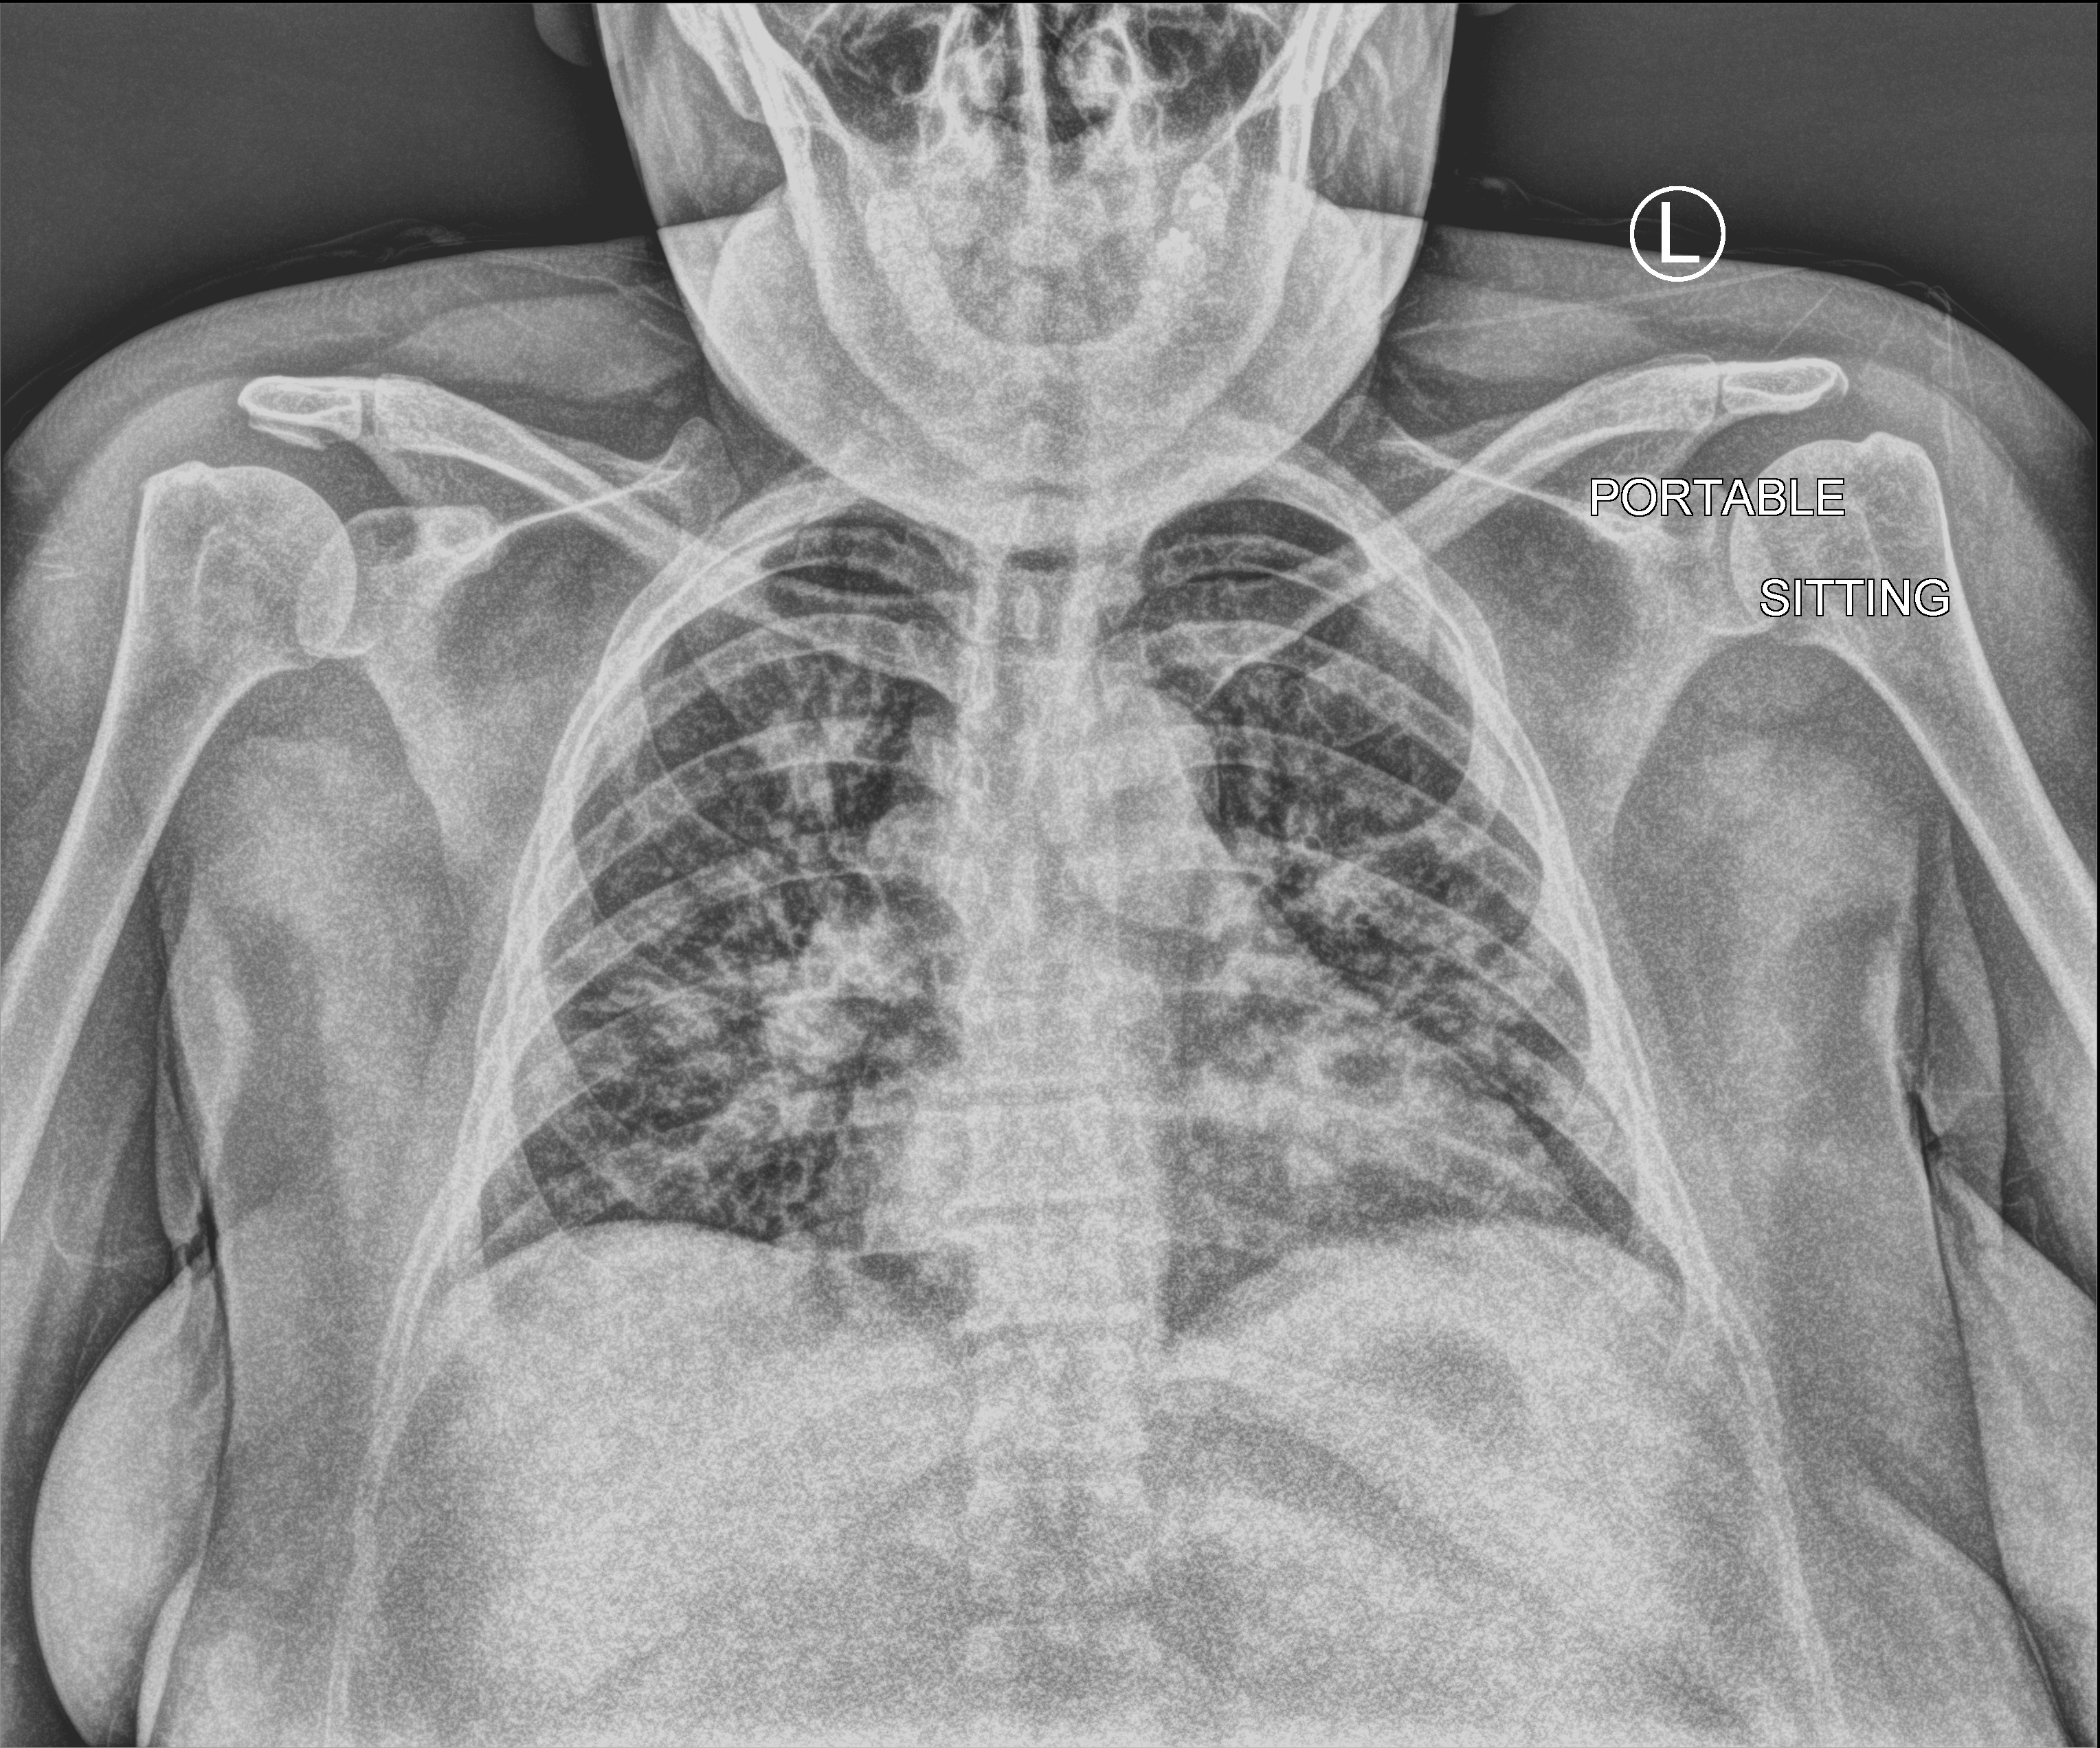
Bedside chest radiograph (computed radiography); anteroposterior (AP) projection. Patient hospitalised with COVID-19; female, aged 18–59 years.
Admission-level facts for this patient (not findings on this image; timing relative to this image not recorded): other chronic lung disease (admission record): no; mechanically ventilated during this hospital stay: yes; chronic kidney disease (admission record): no.